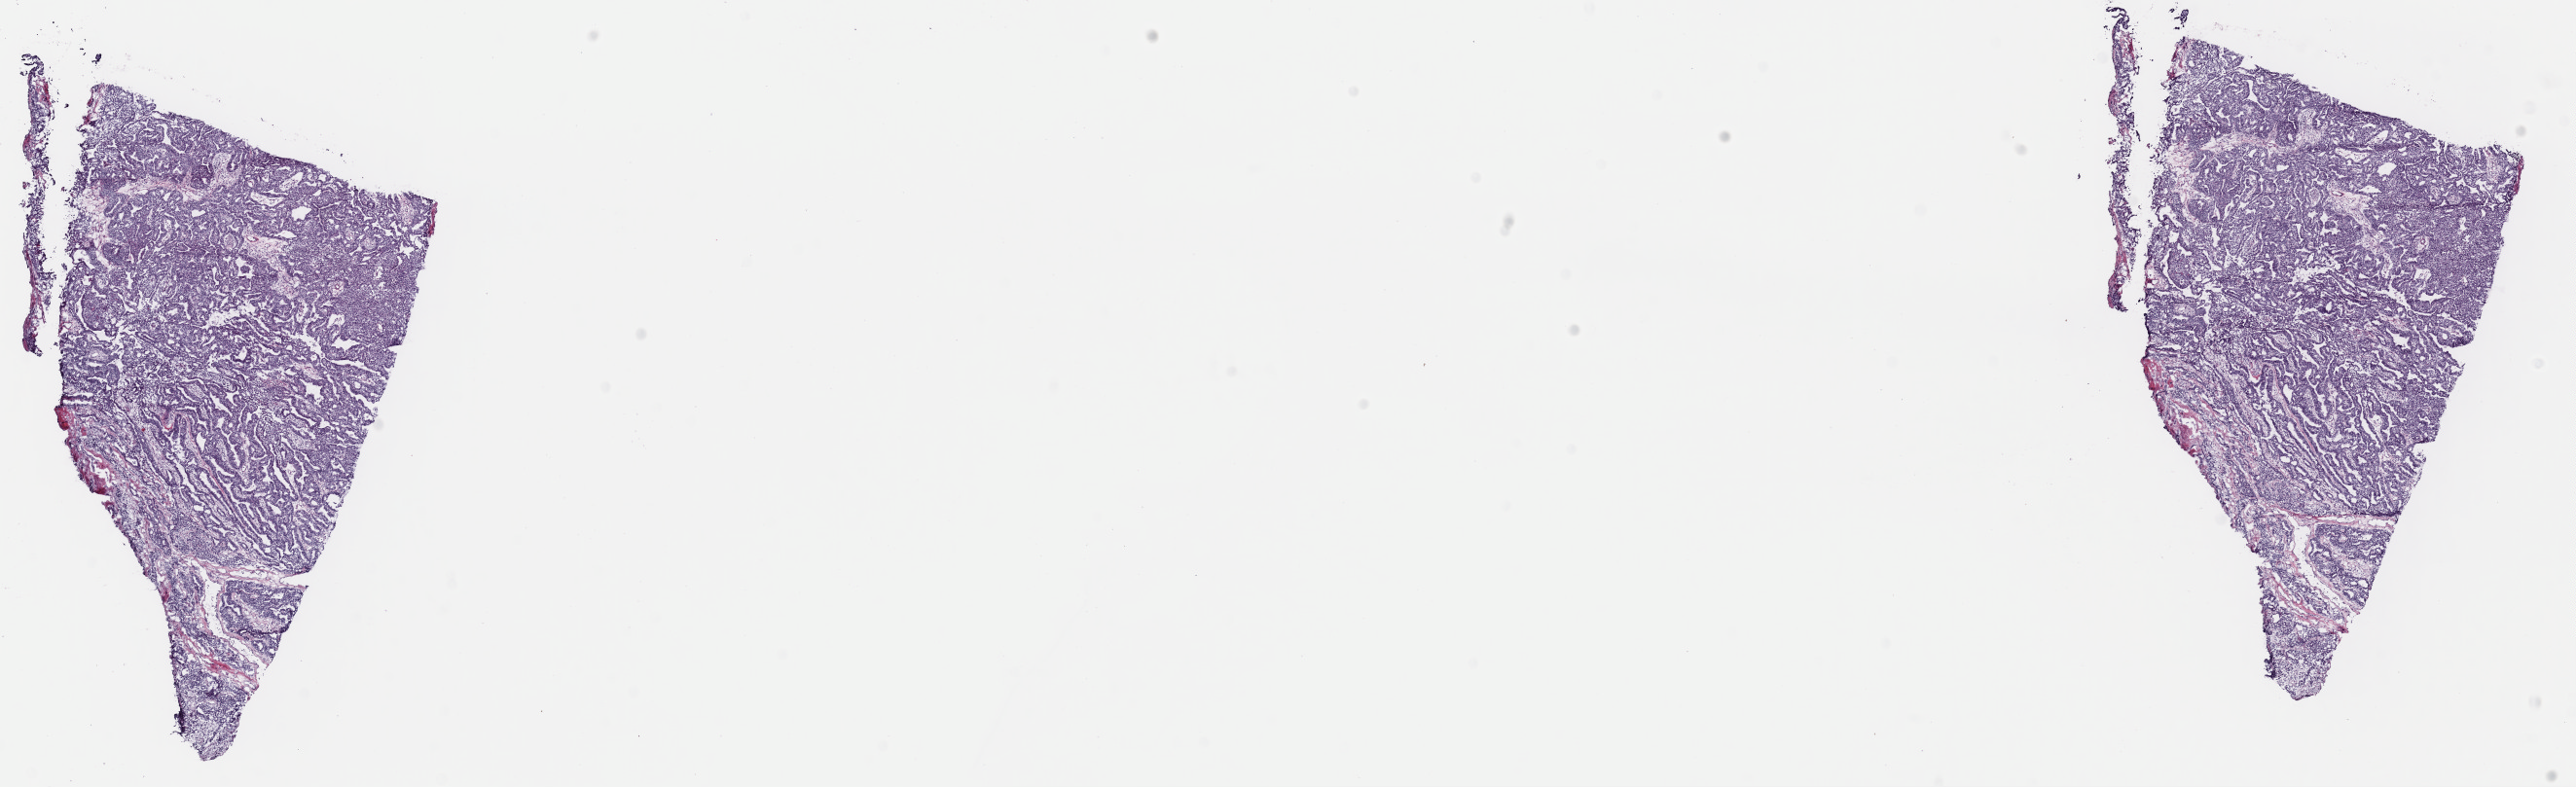
H&E-stained whole-slide image — shown as a low-resolution overview of the whole scanned area (about 20.9 x 6.4 mm, acquisition: 40x scan); frozen section from the top of the tissue portion; primary tumour sample from the uterus. Female, age 81 years at initial diagnosis. Histologic grade: G3 (poorly differentiated). Composition of this section per pathologist review: tumour cells 100%, tumour nuclei 75%, normal cells 0%, stromal cells 0%, necrosis 0%. Inflammatory infiltration, as recorded: lymphocyte infiltration 0%, monocyte infiltration 0%, neutrophil infiltration 0%.
• FIGO stage: IVB
• histologic diagnosis: Endometrioid adenocarcinoma, NOS (endometrium)